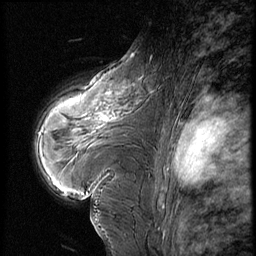
Breast MRI (dynamic contrast-enhanced), one sagittal slice. 3 images stored at this slice position (order not interpretable as contrast timing). 1.5 T. TE 4.2 ms, TR 8.9 ms. 256 × 256 image matrix. Patient: female, 39 years. From the clinical record (not read from this slice): setting: breast cancer imaged before/during neoadjuvant chemotherapy; receptor status: HER2-positive.
Structures marked on this image (semi-automatic segmentation, software-assisted and operator-edited):
- analysis volume of interest (the breast-tissue region the enhancement analysis was run in; not a lesion): bounding box <72,79,141,135> (left, top, right, bottom; pixels)
- tumour enhancement mask (voxels above the 140 % enhancement threshold inside the analysis volume of interest): <100,120,102,122>